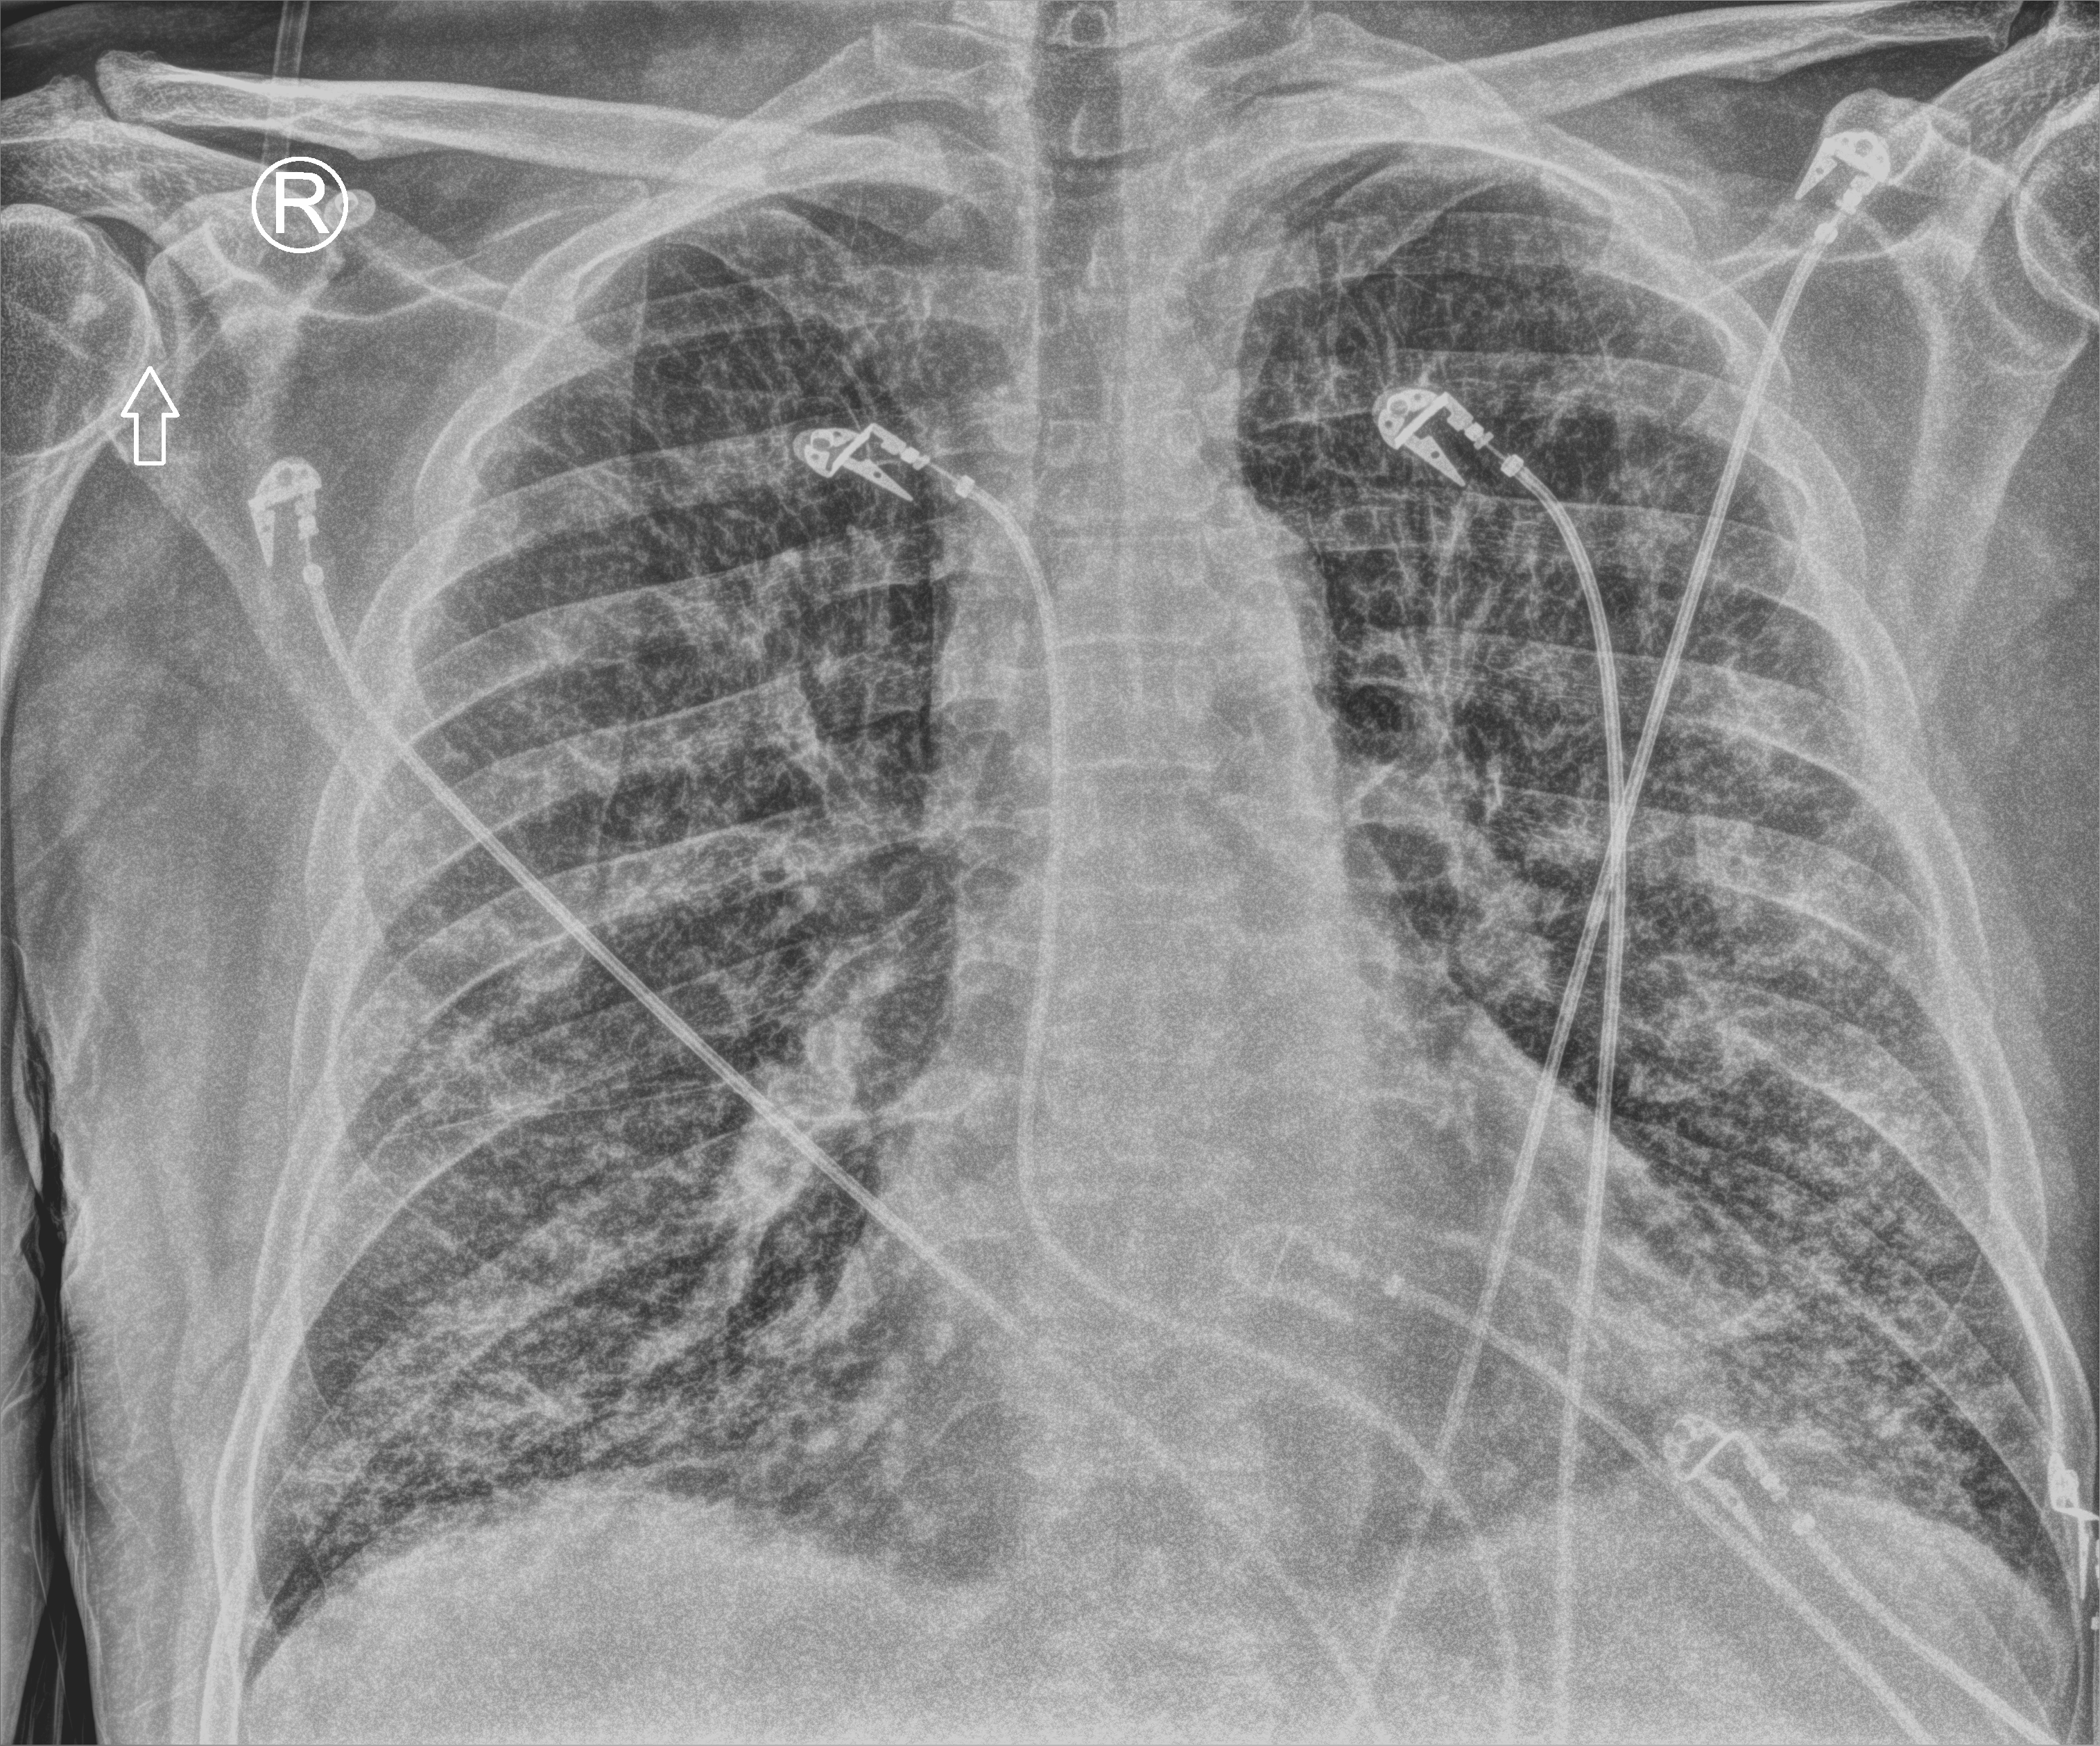
Chest X-ray (portable). Patient hospitalised with COVID-19, aged 18–59 years.
Admission-level facts for this patient (not findings on this image; timing relative to this image not recorded):
- mechanically ventilated during this hospital stay: no